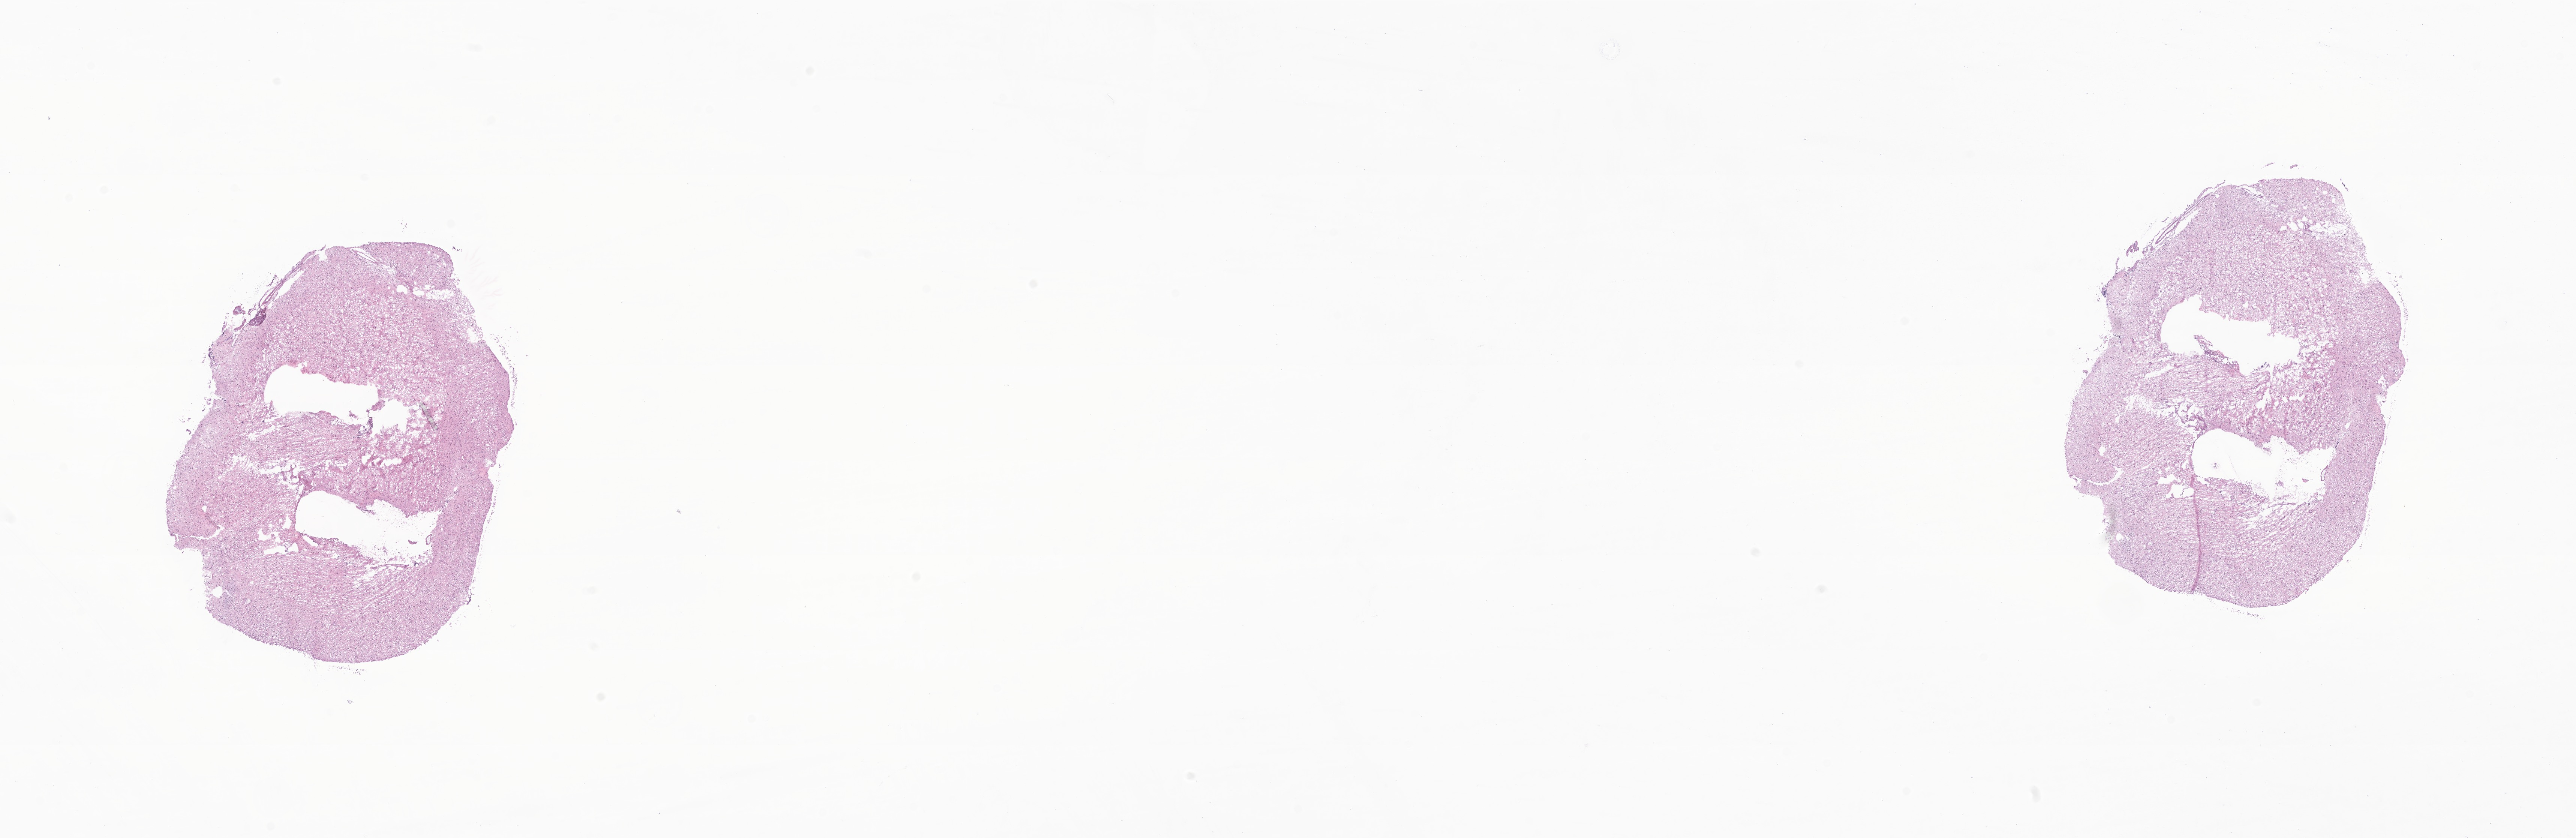
Digitized haematoxylin and eosin-stained section of tumor tissue from the brain — low-resolution overview of the scanned area, about 29.0 x 9.4 mm; frozen section. Male patient, age 138 months (11 years 6 months).
Recorded diagnosis: Glioma, malignant.